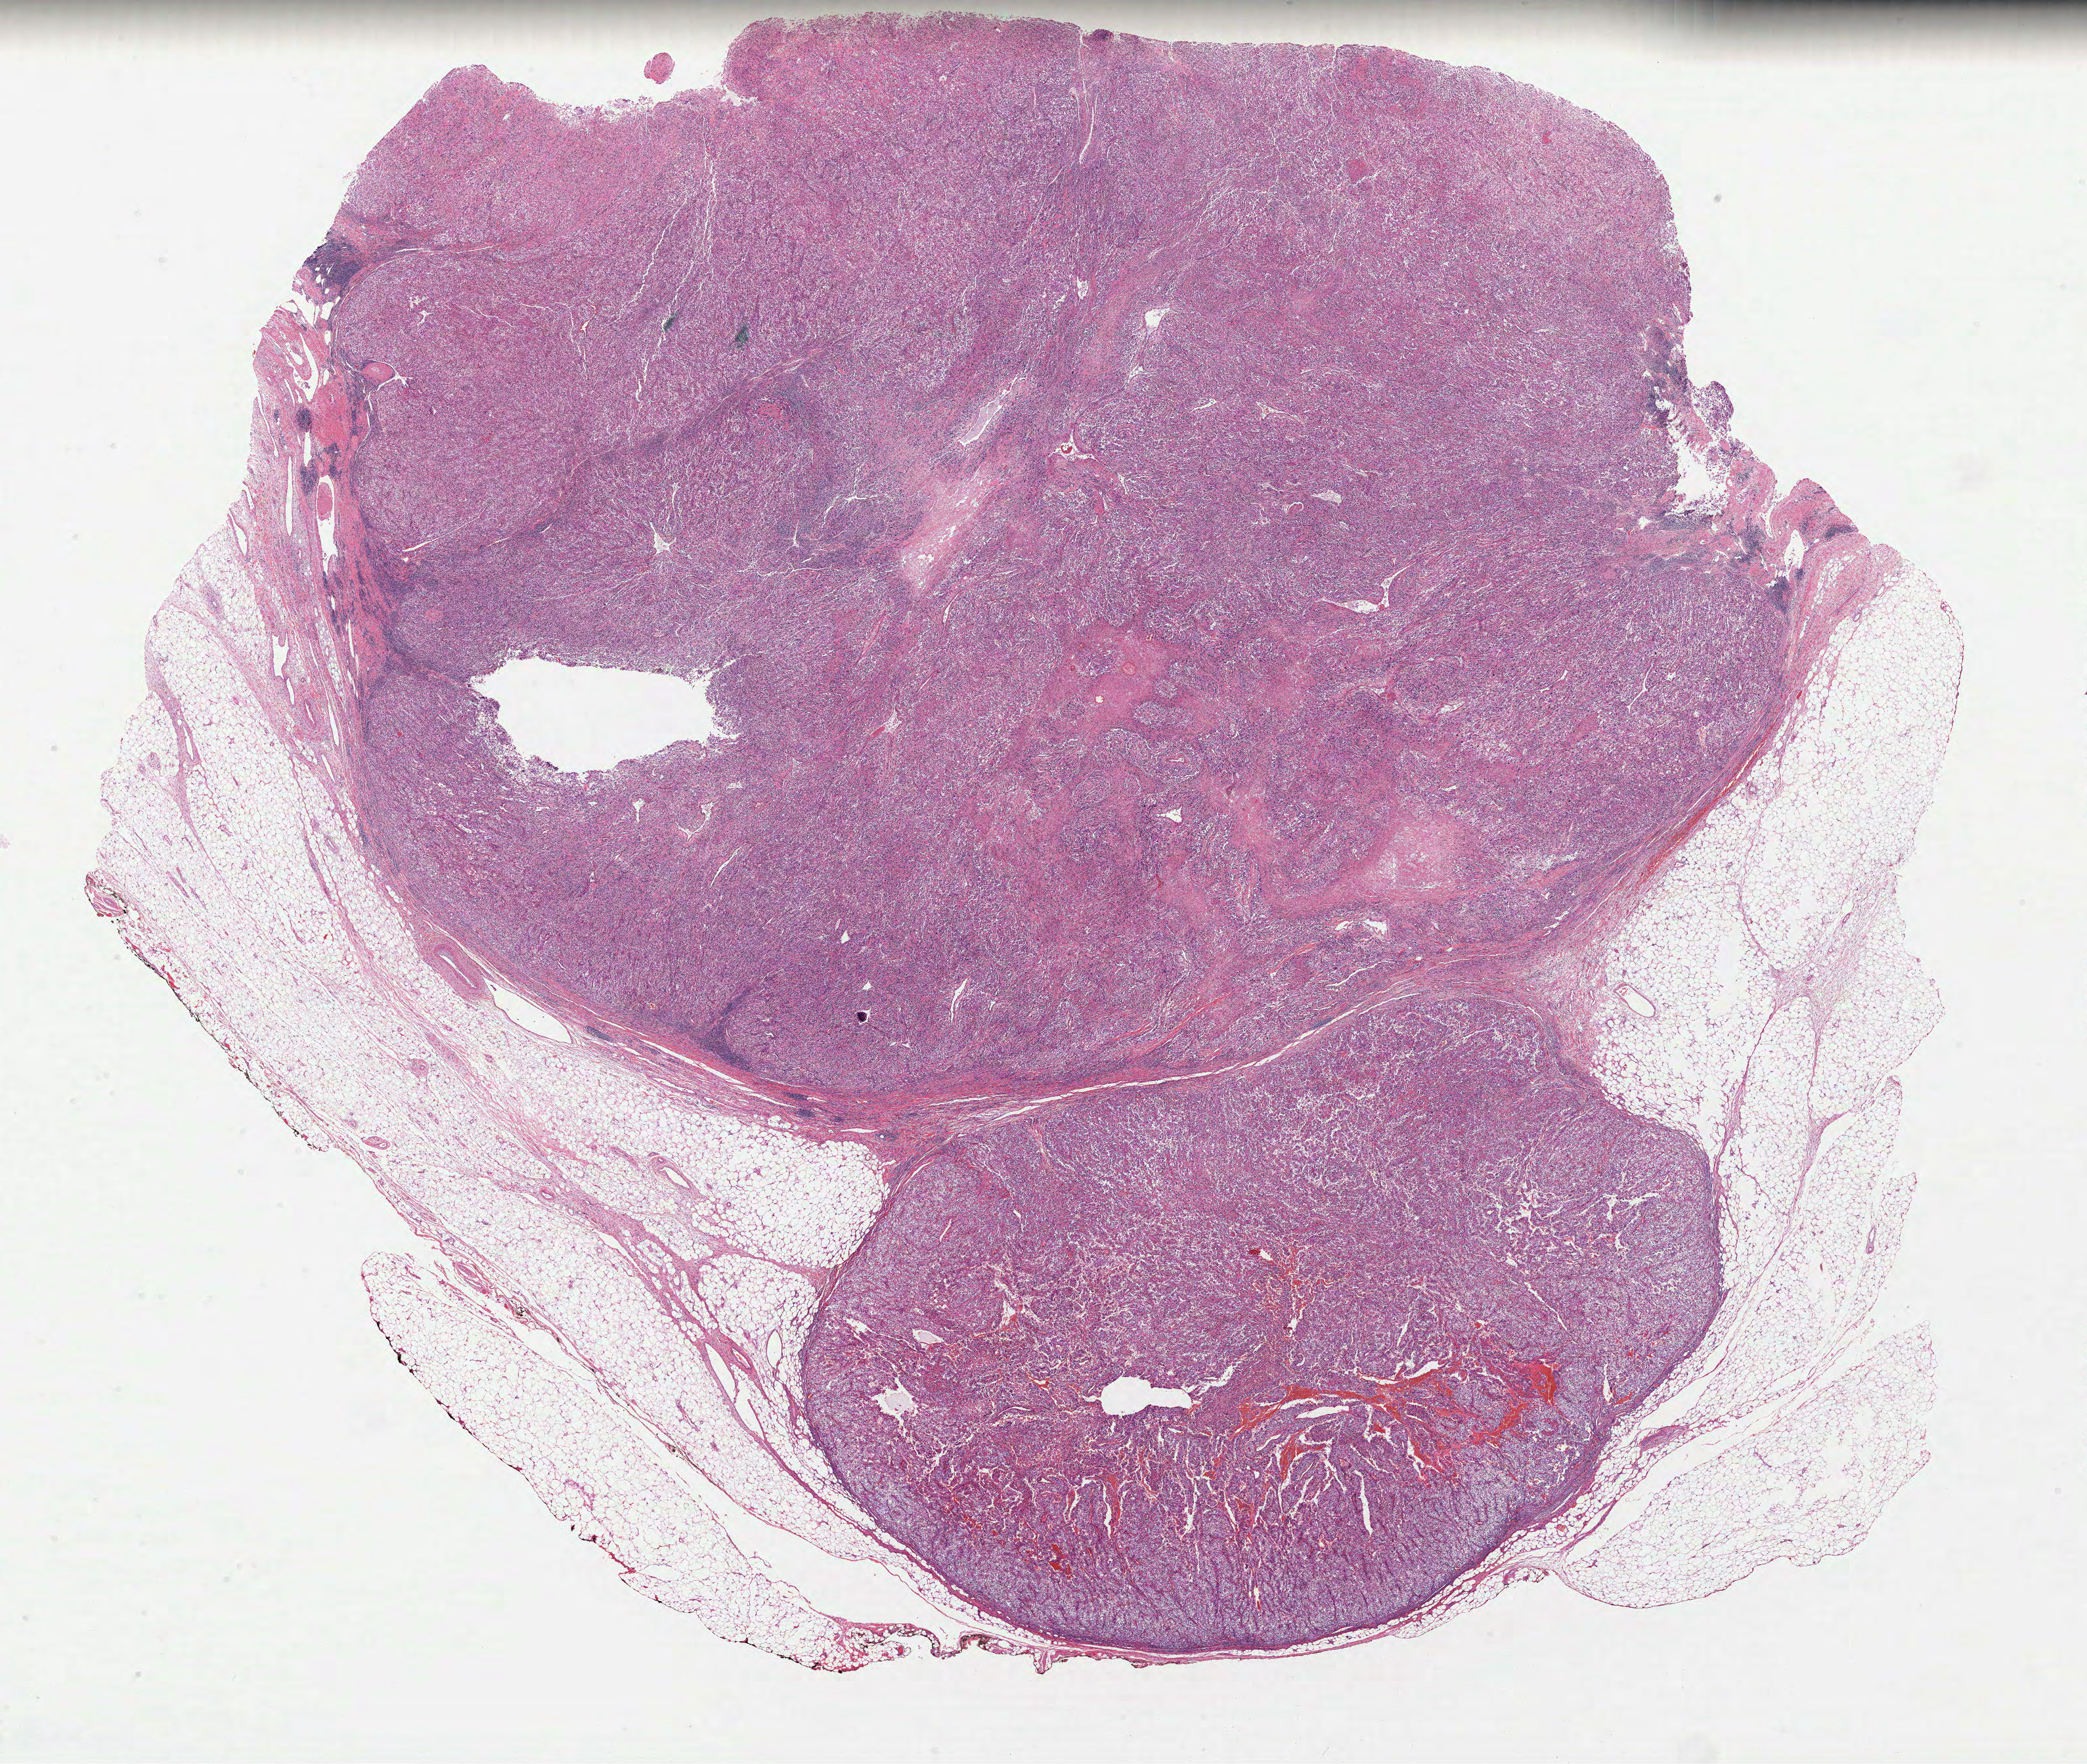
Whole-slide histology image, H&E, low-resolution overview of the scanned area, about 25.6 x 21.7 mm. Formalin-fixed paraffin-embedded (FFPE) diagnostic section. Sample: primary tumour, kidney. Male patient; age at initial diagnosis 84 years. Histologic grade: G4 (undifferentiated).
Diagnosis: Clear cell adenocarcinoma, NOS. AJCC pathologic stage: IV. Laterality: left. TNM: T3b NX M1.